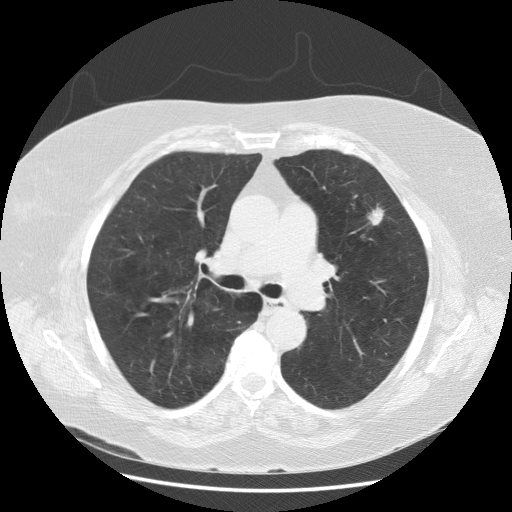
Axial slice from a low-dose chest CT screening exam; second annual screen; lung window (W 1500 / L -600 HU); standard (soft-tissue) reconstruction kernel (STANDARD); 512 × 512 image matrix. Female, age 68 years at enrolment. Current smoker at enrolment.
Lesion marked by an expert reader, bounding box (x1, y1, x2, y2) in pixels: (361, 202, 396, 232). The screening reader recorded 2 non-calcified nodules or masses ≥4 mm on this exam; which of them this box marks is not recorded. Later outcome: lung cancer diagnosed 90 days after this screen — large cell carcinoma, NOS, left upper lobe, undifferentiated (G4), stage IA (AJCC 6th edition), 10 mm at pathology.